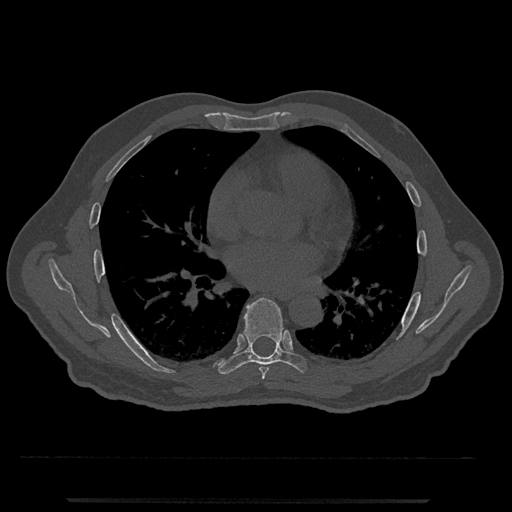
CT including the spine, one axial slice. Slice 696 of 797 in the series (ordered by position). Bone window (W 1800 / L 400 HU). 0.5 mm slice thickness. 512 × 512 image matrix, field of view 419 × 419 mm. Male patient, age 63 years. From the clinical record (not read from this slice): primary cancer: prostate.
Outlined on this slice (semi-automatic segmentation, software-assisted and operator-edited):
- T6 vertebra: bounding box (x1, y1, x2, y2) in pixels: (259, 367, 269, 380)
- T7 vertebra: (217, 298, 308, 375)